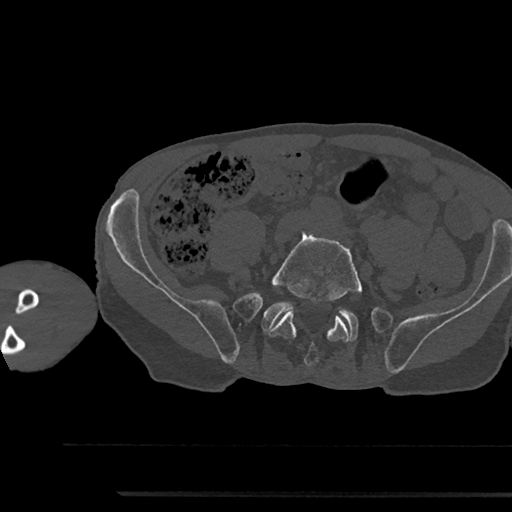
CT including the spine, one axial slice. Slice 334 of 797 in the series (ordered by position). Reconstruction kernel Br40s/3. Bone window (W 1800 / L 400 HU). 0.5 mm slice thickness. 512 × 512 image matrix, field of view 367 × 367 mm. Patient: male, 79 years. From the clinical record (not read from this slice): primary cancer: prostate.
Annotated regions visible in this slice (semi-automatic segmentation, software-assisted and operator-edited):
- L5 vertebra: bounding box [x1, y1, x2, y2] px = [268, 231, 362, 366]